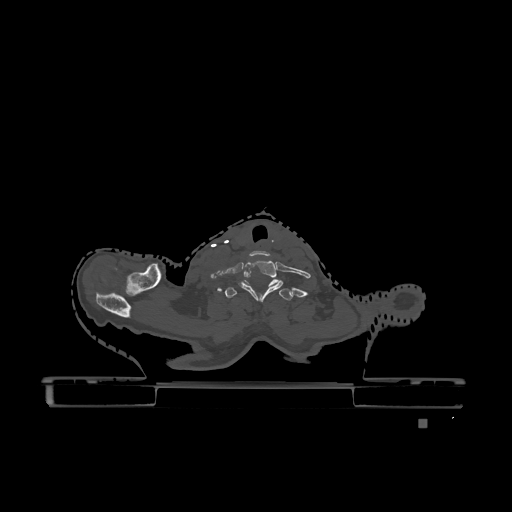
CT including the spine, one axial slice. Position 1020 of 1317 along the scan axis. Bone window (W 1800 / L 400 HU). 512 × 512 image matrix, field of view 500 × 500 mm. Patient: female, 74 years. Case-level facts recorded for this patient, not image findings: primary cancer: lung; vertebrae with lytic lesions (as recorded): T1, T4, T5, T6, L4, L5.
Annotated regions visible in this slice (semi-automatically segmented with operator editing):
- T1 vertebra: bounding box (x1, y1, x2, y2) in pixels: (225, 280, 293, 300)